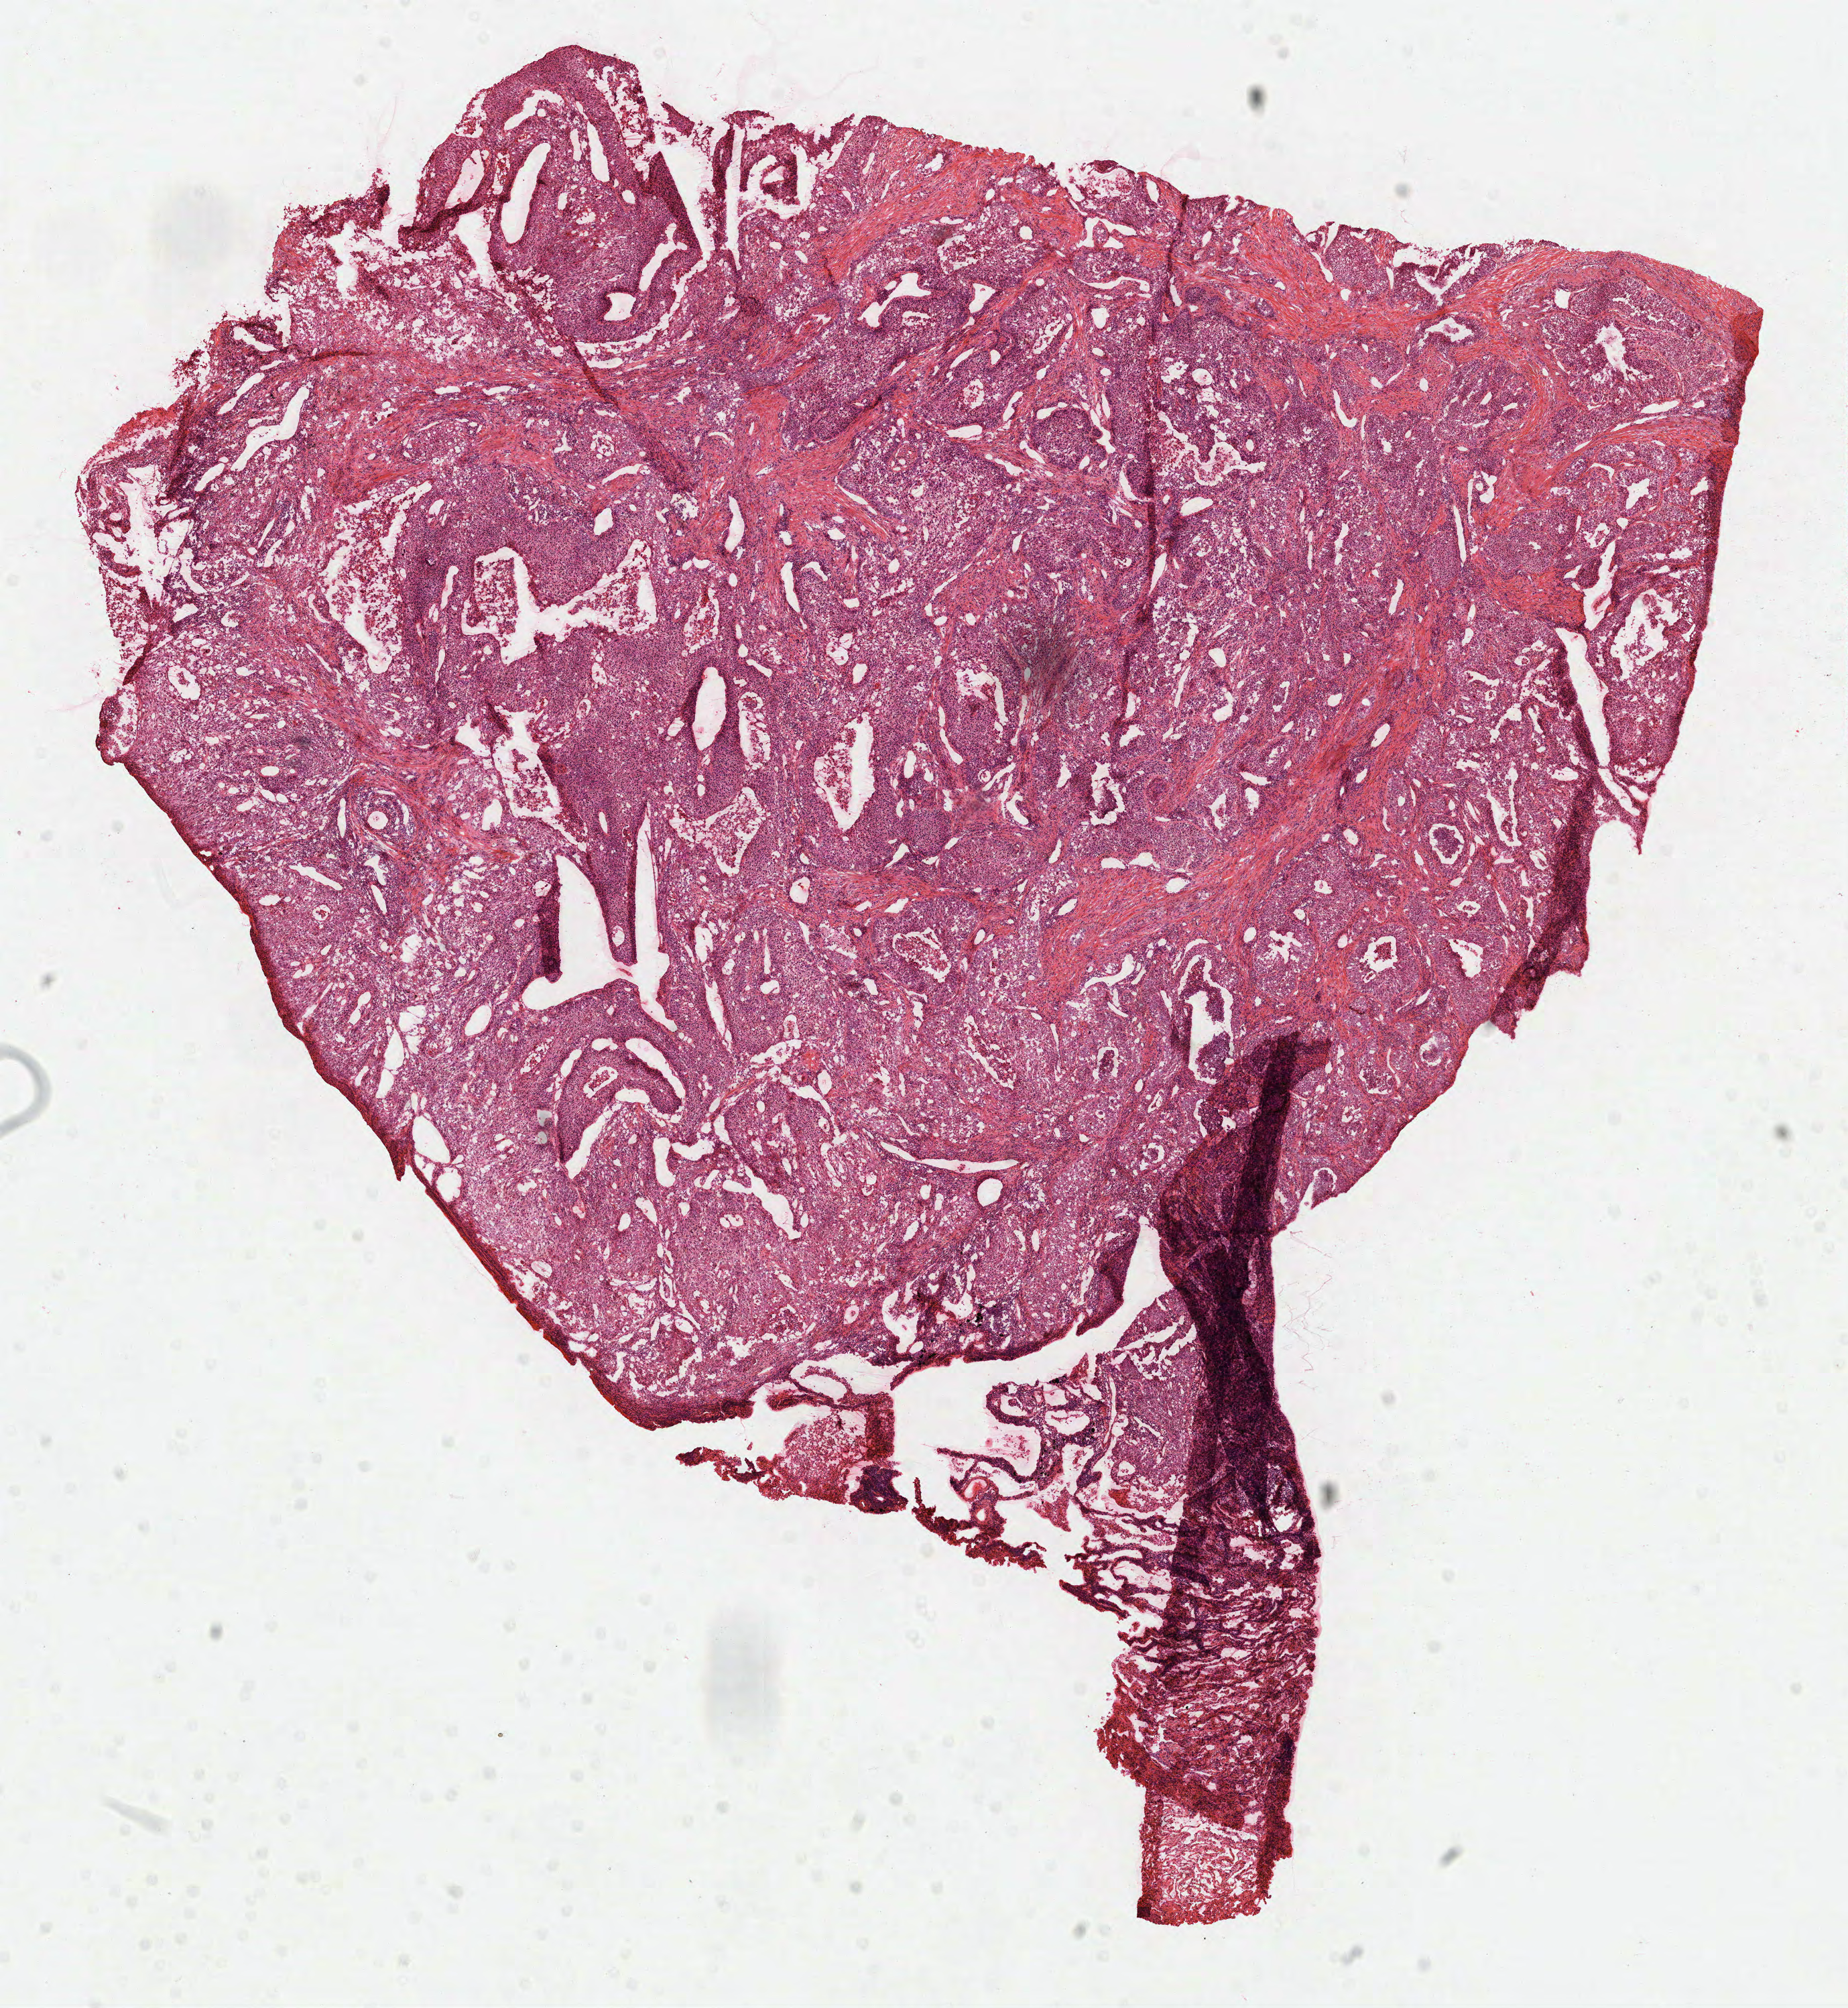
Whole-slide histology image, H&E — shown as a low-resolution overview of the whole scanned area (about 11.1 x 12.1 mm, from a 40x scan), formalin-fixed paraffin-embedded (FFPE) diagnostic section, sample: primary tumour, lung. Female patient; age at initial diagnosis 60 years.
Histologic diagnosis: Squamous cell carcinoma, NOS (upper lobe, lung).